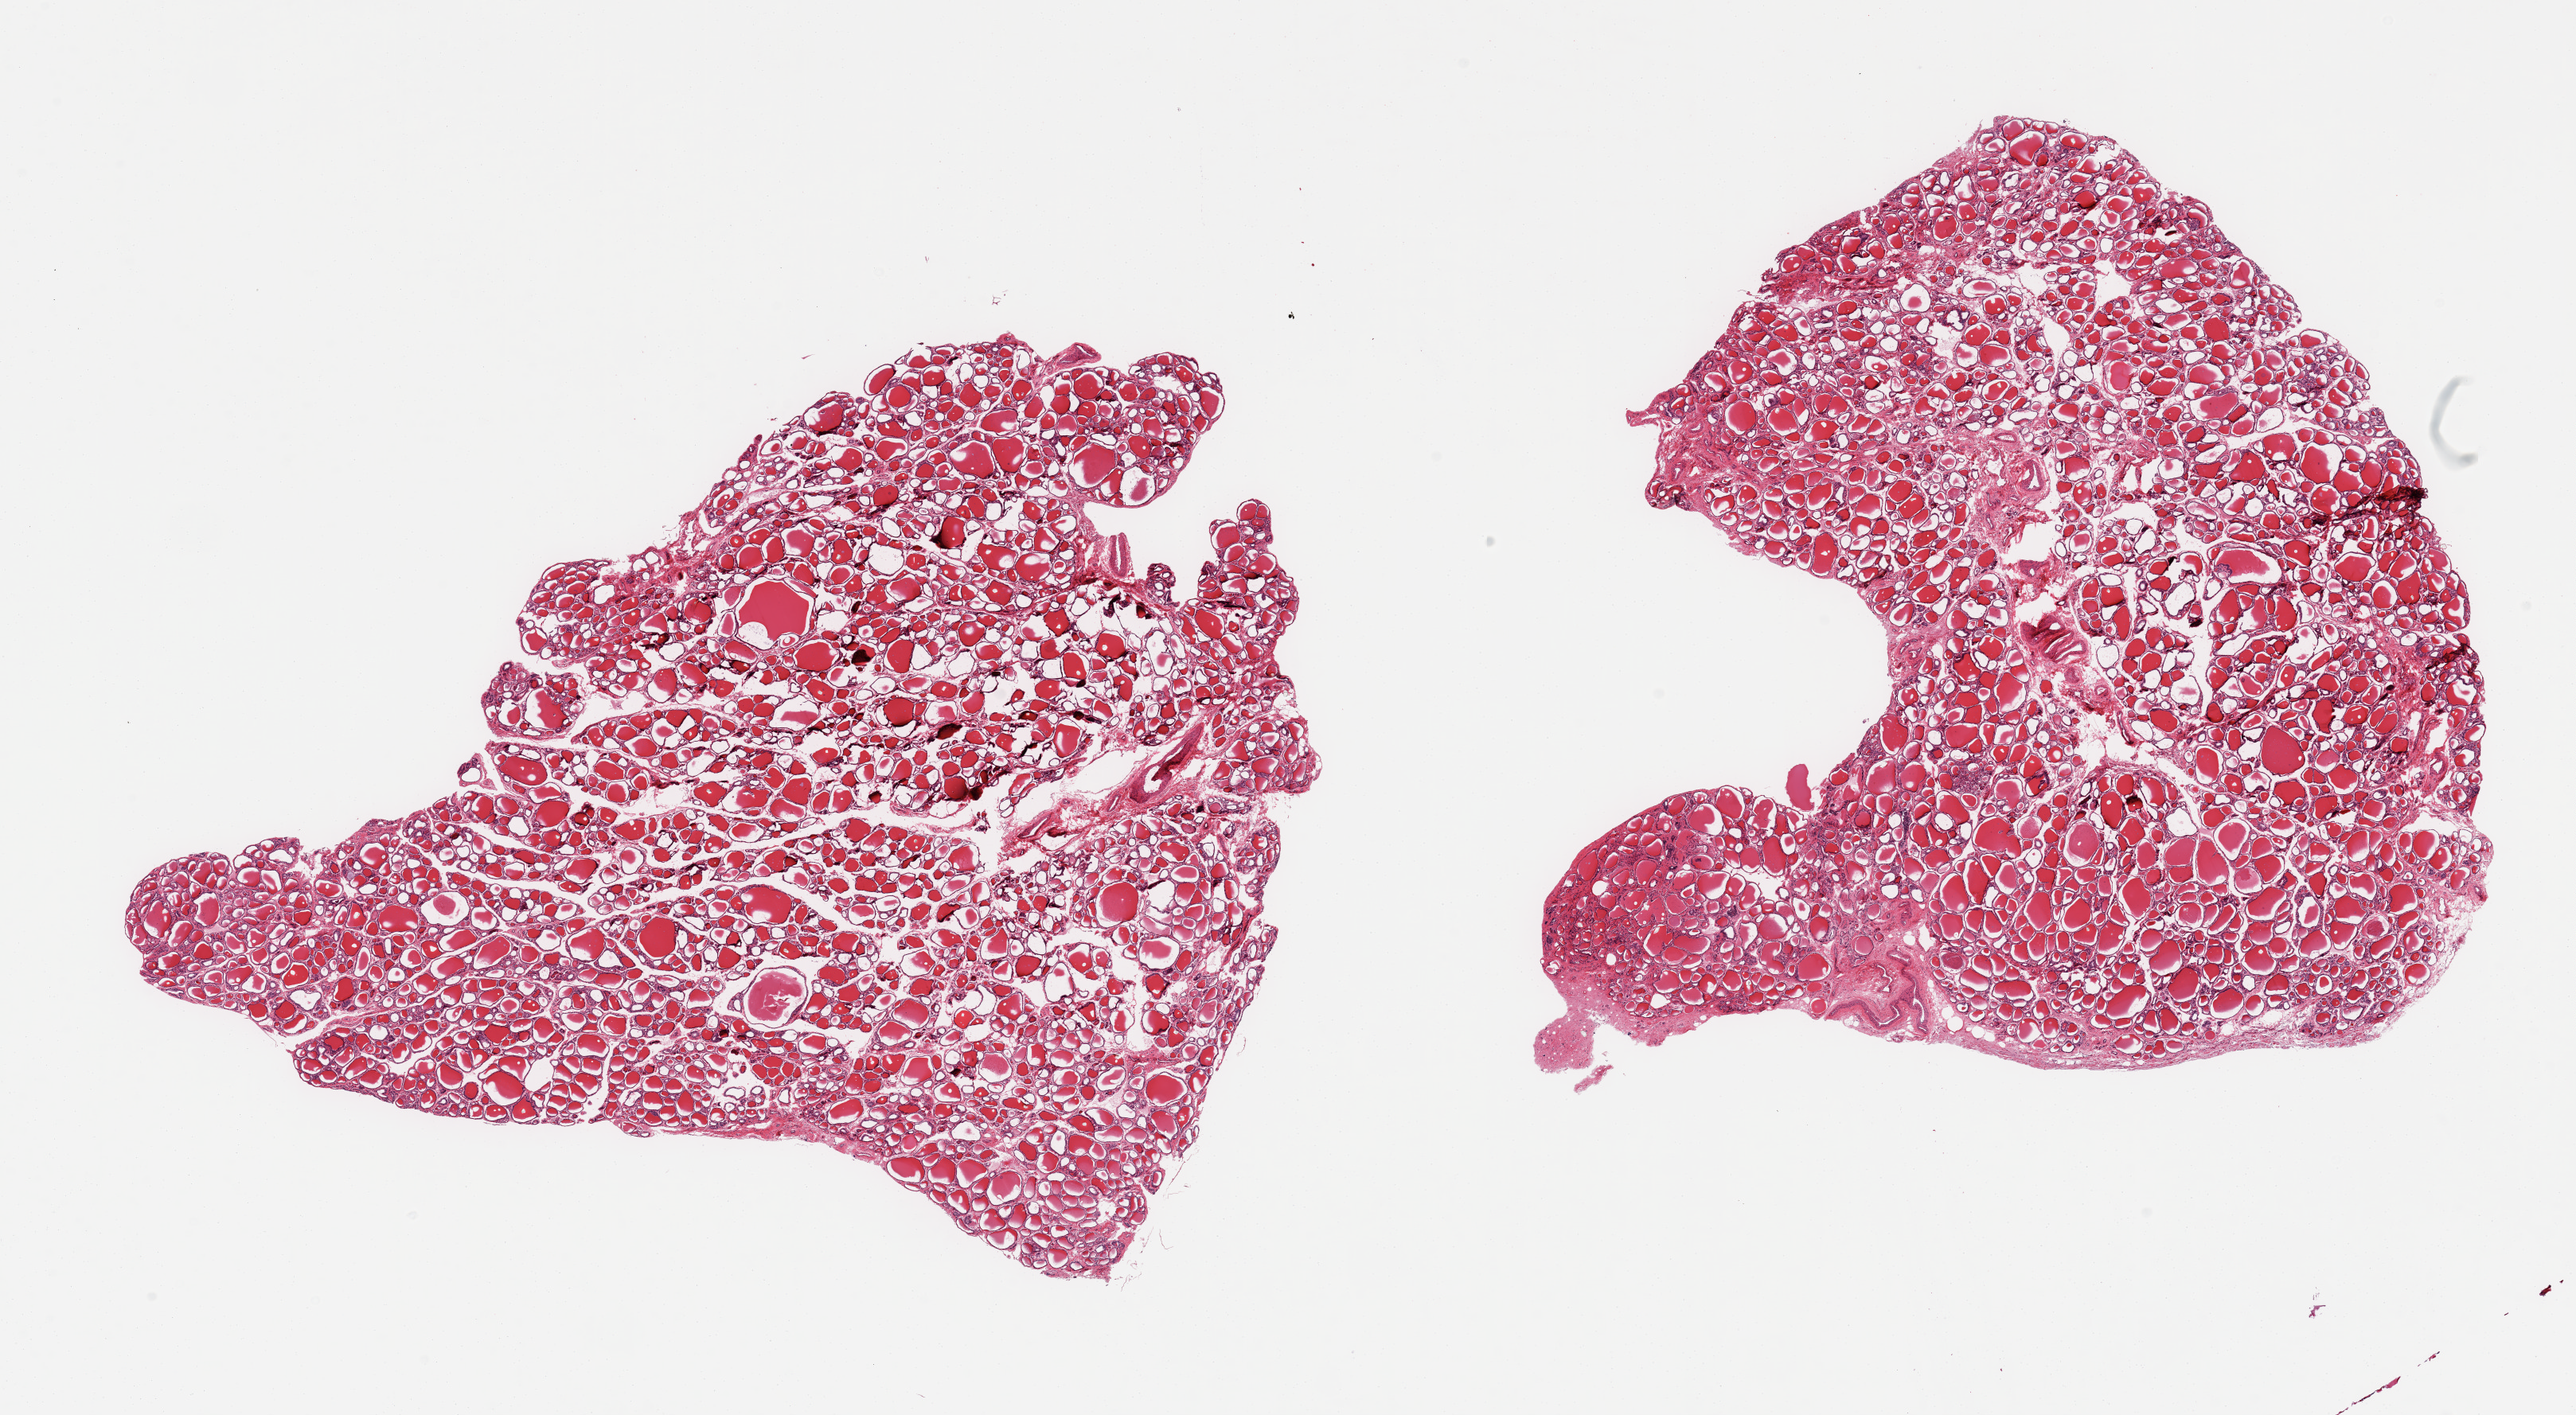
Whole-slide image, H&E stain — whole scanned area (about 25.6 x 14.1 mm) shown as a low-resolution overview. PAXgene-fixed paraffin-embedded (PFPE) section. Target tissue: thyroid. Donor tissue sample. Donor sex: male.
Review note (as recorded): 2 pieces; <5% fibrovascular content.